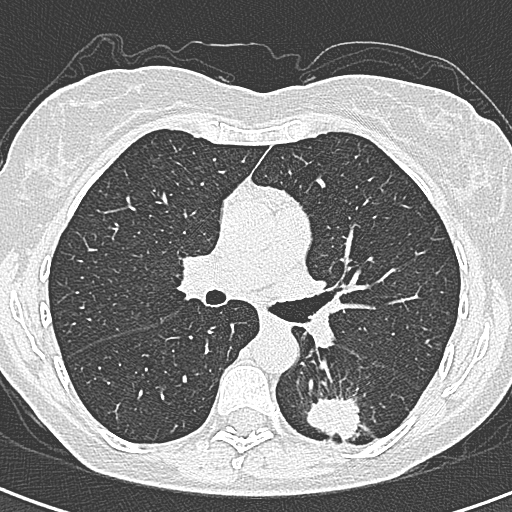
Chest CT (low-dose screening protocol), one axial image; baseline screening round; lung window (W 1500 / L -600 HU); 1 mm slice thickness; lung (sharp) reconstruction kernel (B80f); slice 130 of 328 in the series. Female, age 58 years at enrolment.
- Lesion marked by an expert reader, bounding box [x1, y1, x2, y2] px = [295, 388, 365, 455].
- The screening reader recorded 2 non-calcified nodules or masses ≥4 mm on this exam (left lower lobe, right lower lobe); which of them this box marks is not recorded.
- Lung cancer was diagnosed 22 days after this screen: adenocarcinoma, NOS, left lower lobe, moderately differentiated (G2), stage IA (AJCC 6th edition), 25 mm at pathology.